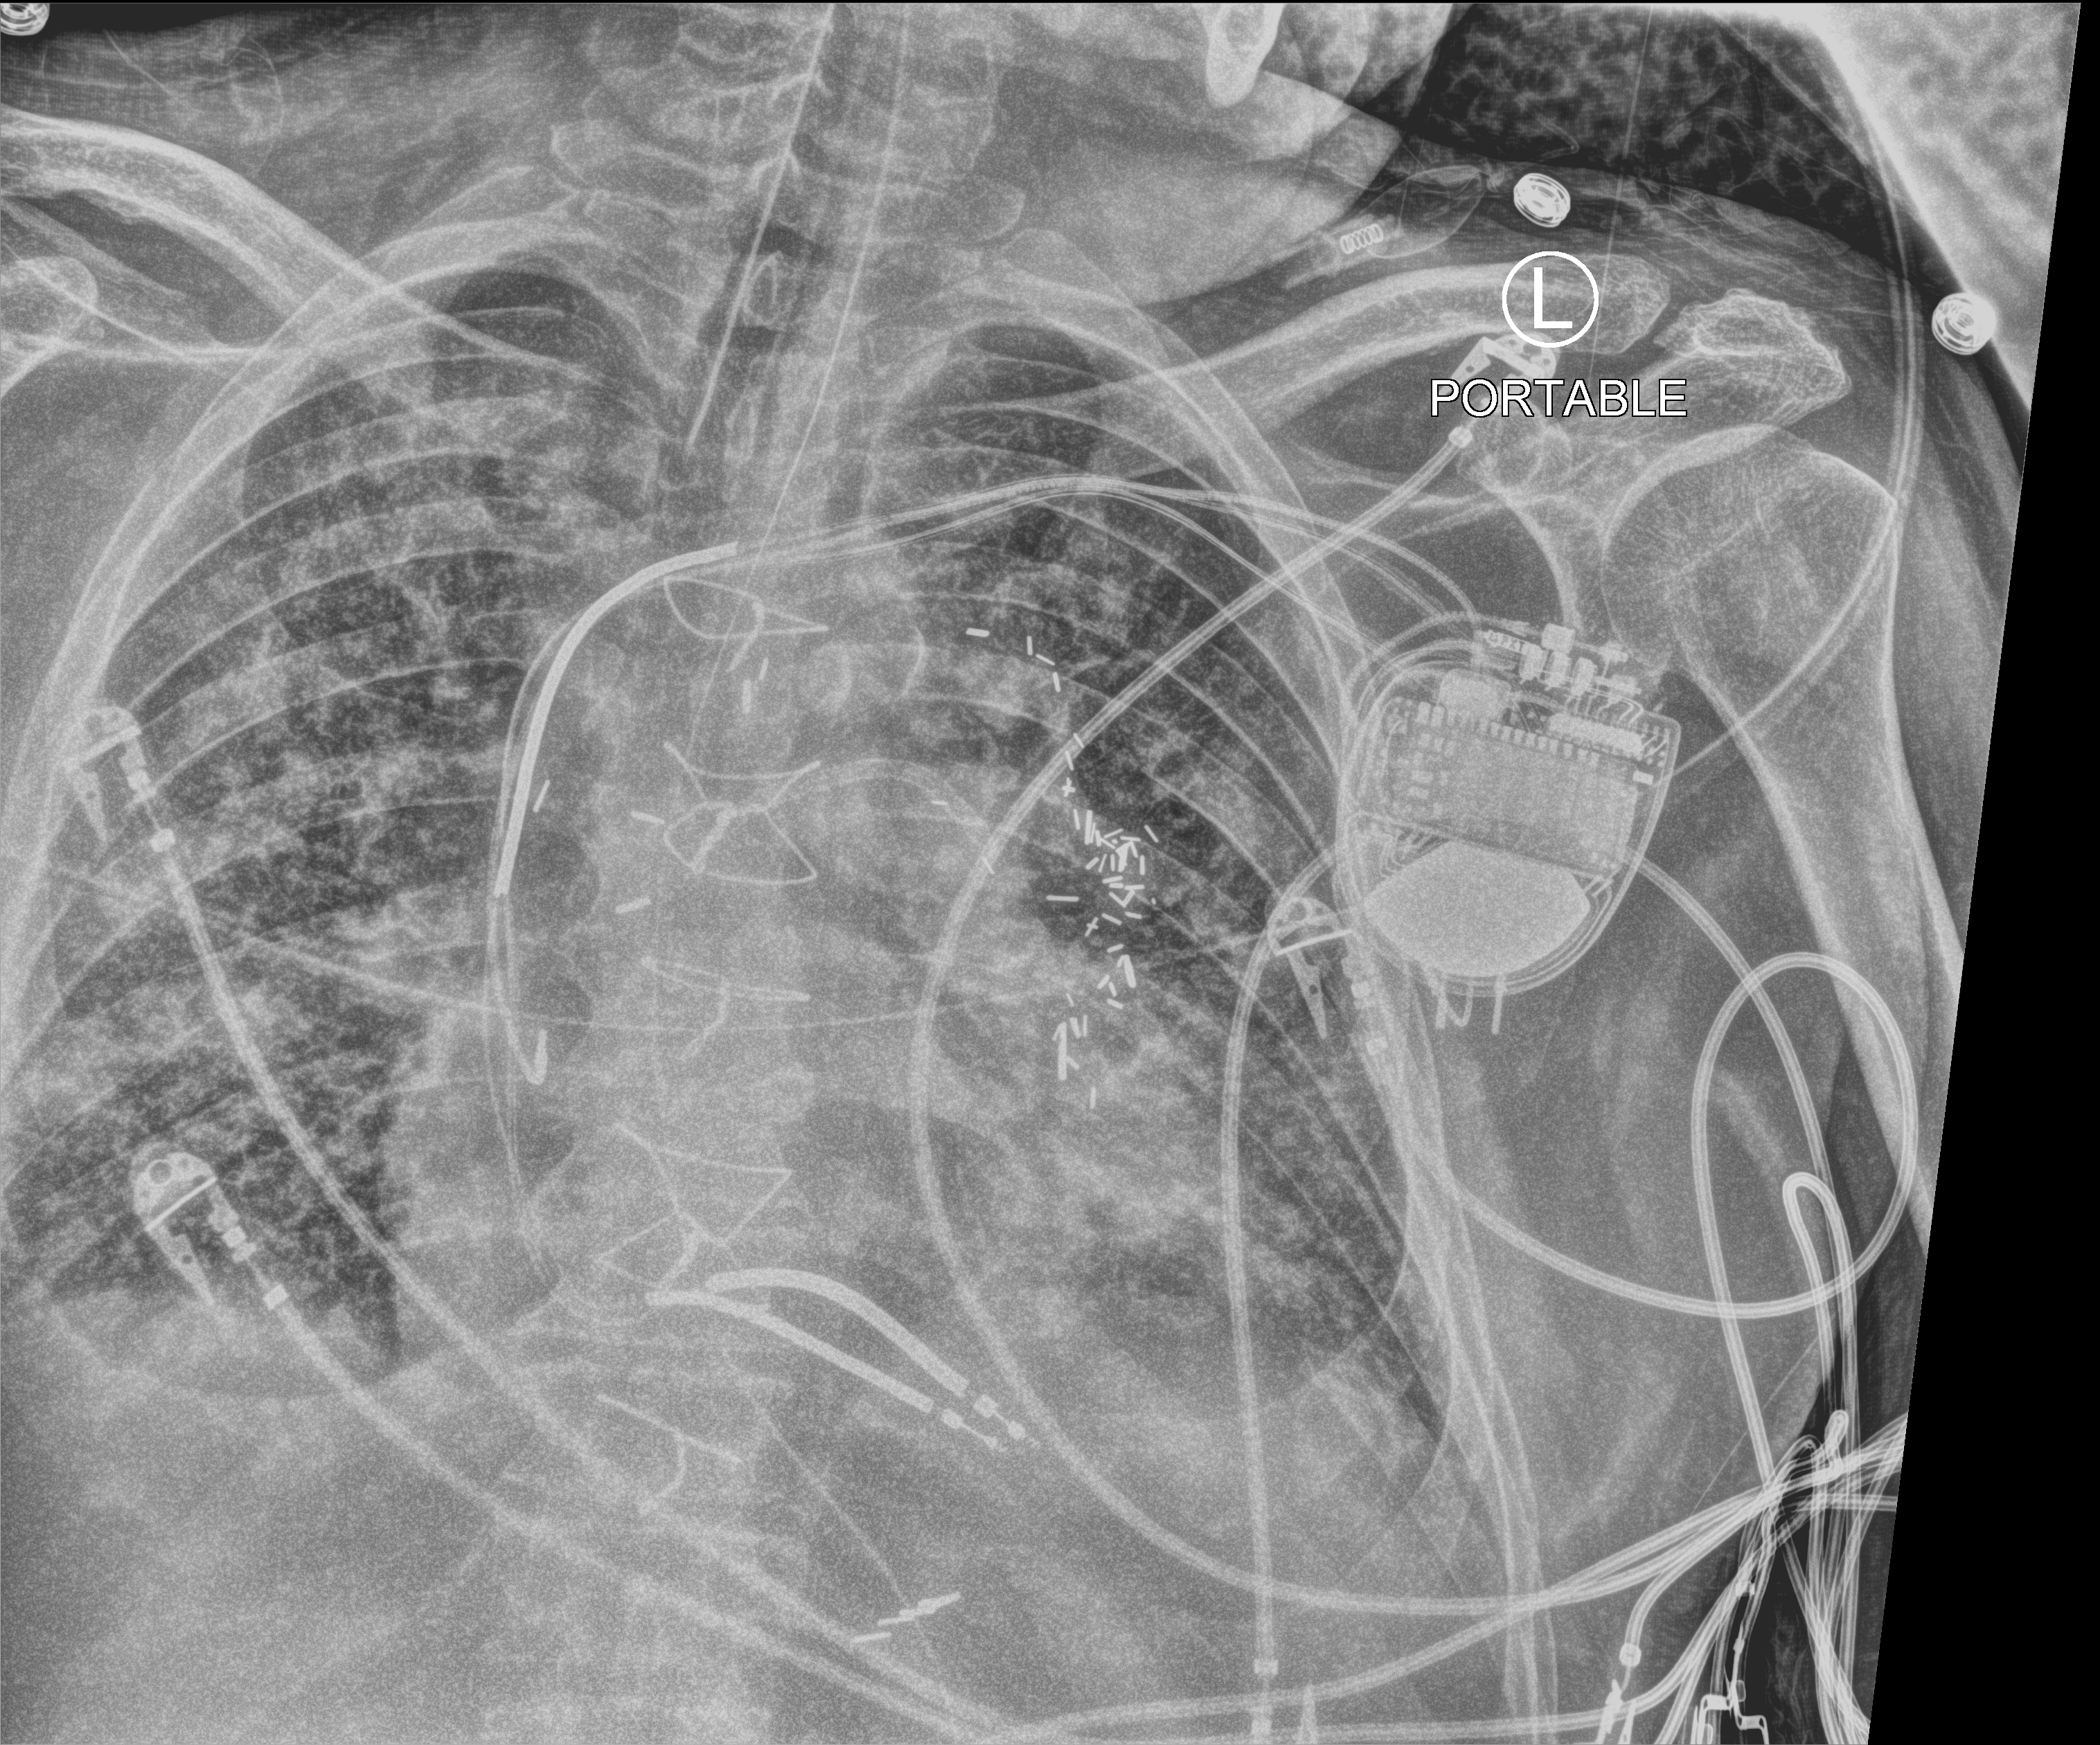
Chest X-ray (portable), anteroposterior (AP) projection. Patient hospitalised with COVID-19; male, aged 60–74 years.
Hospital-stay facts (about this admission, not read from this image; timing relative to this image not recorded): mechanically ventilated during this hospital stay: yes; other chronic lung disease (admission record): no.